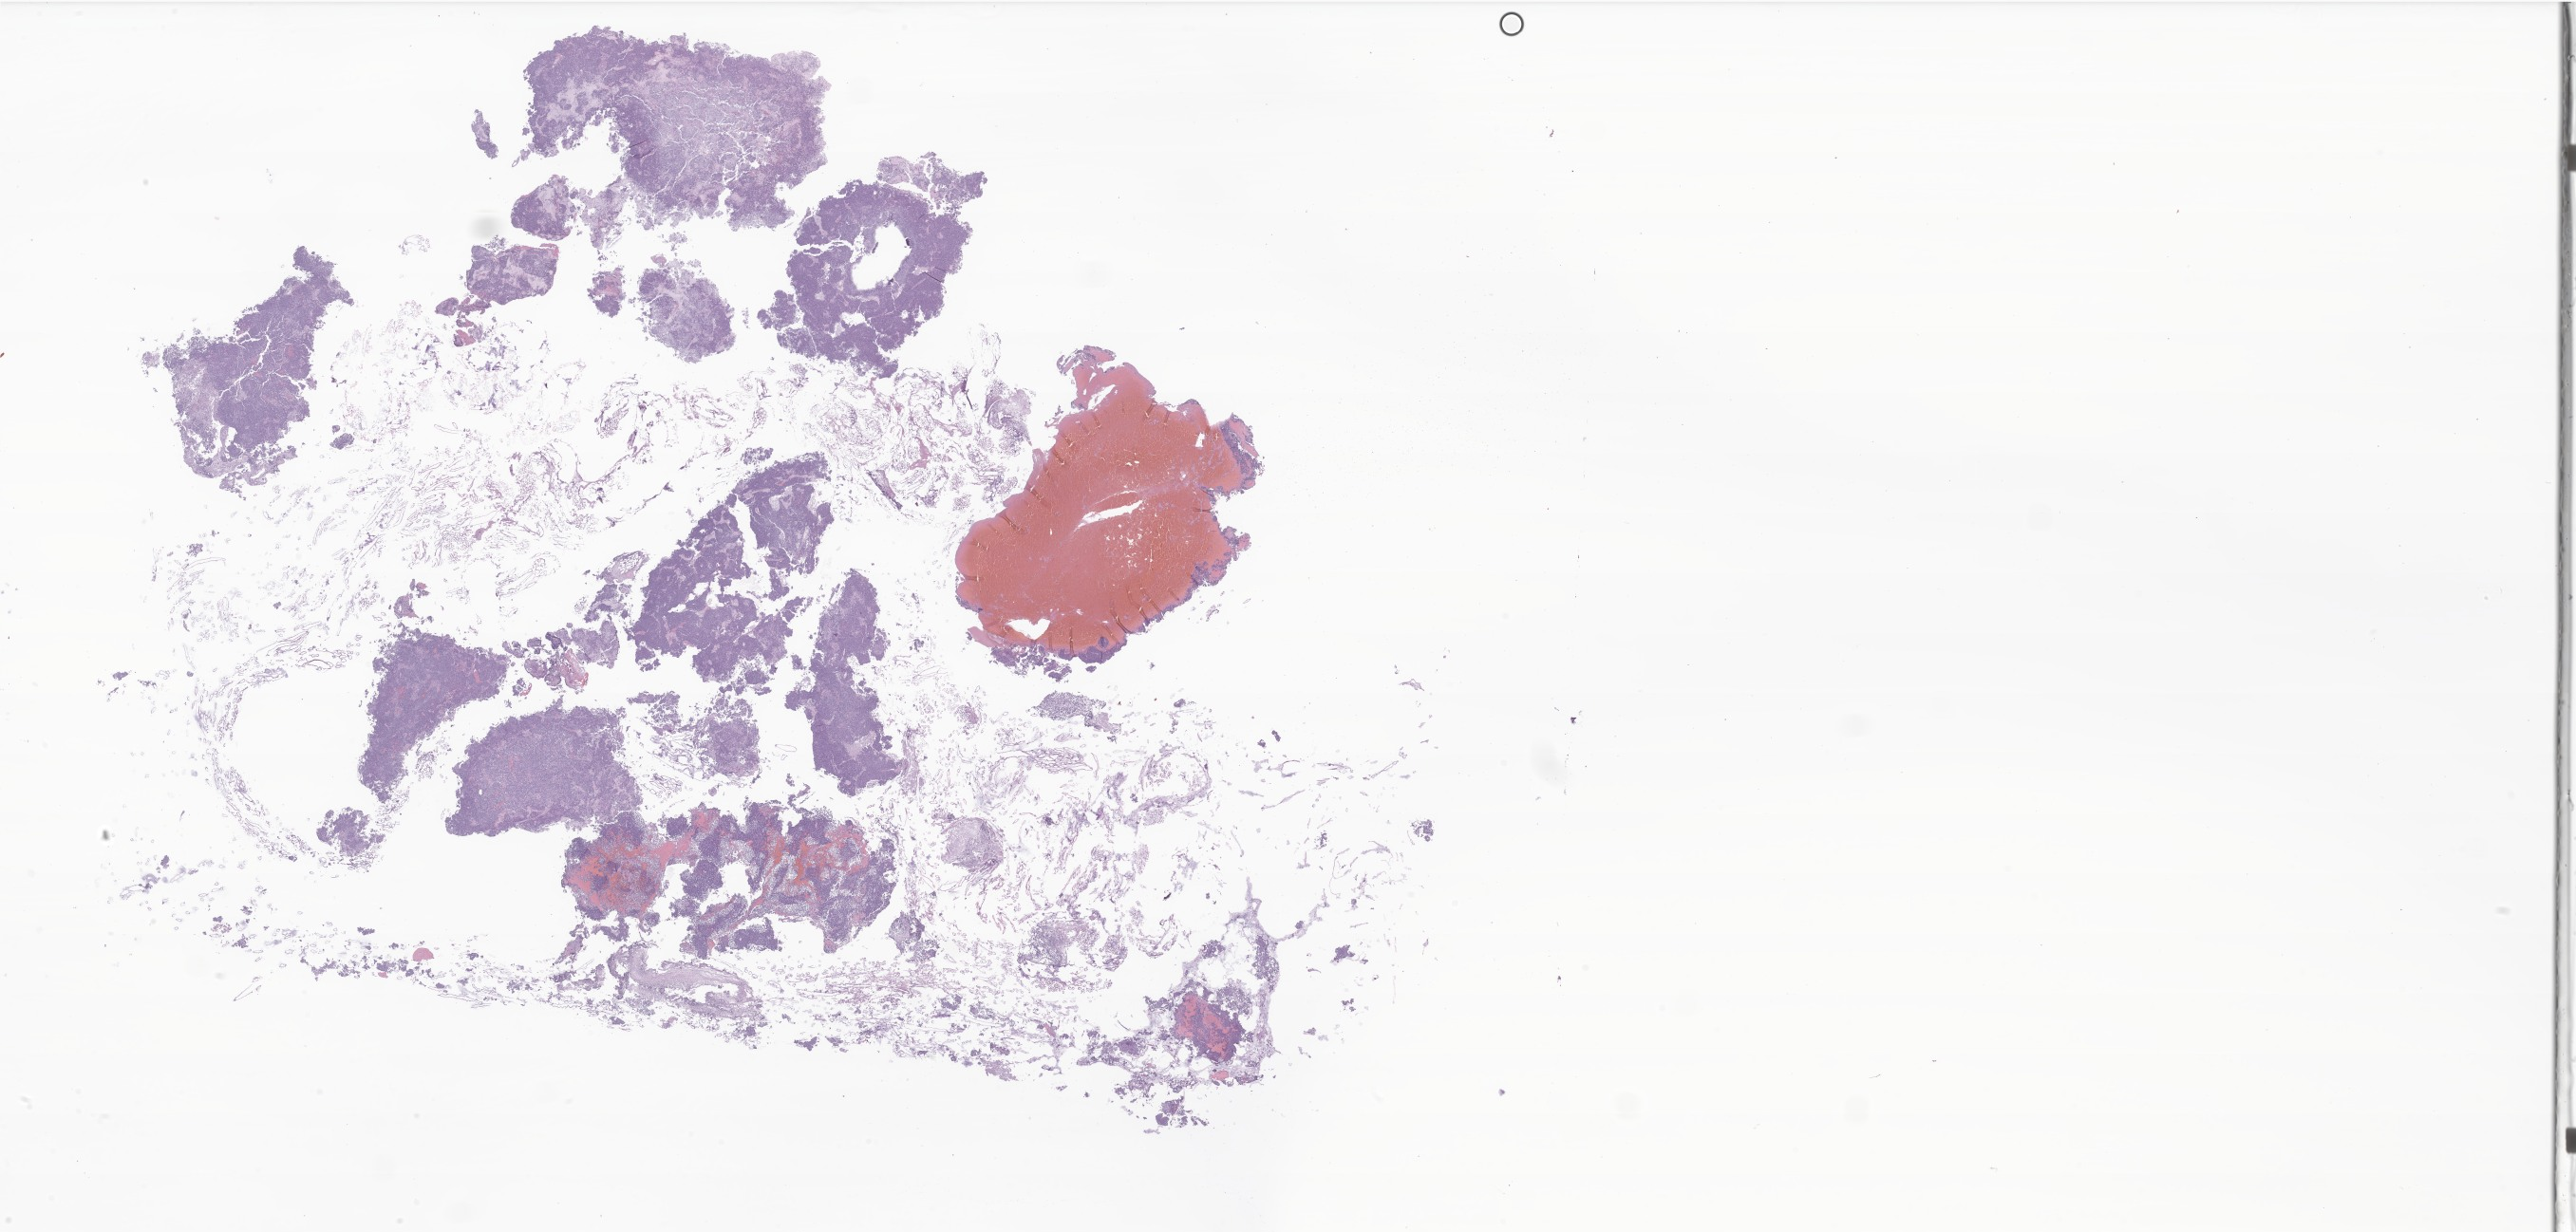
Whole-slide image, H&E stain of tumor tissue from the brain, a low-resolution overview of the entire scanned area, about 45.8 x 21.9 mm; formalin-fixed paraffin-embedded section. Patient: male, age 106 months (8 years 10 months).
• diagnosis: Neoplasm, malignant